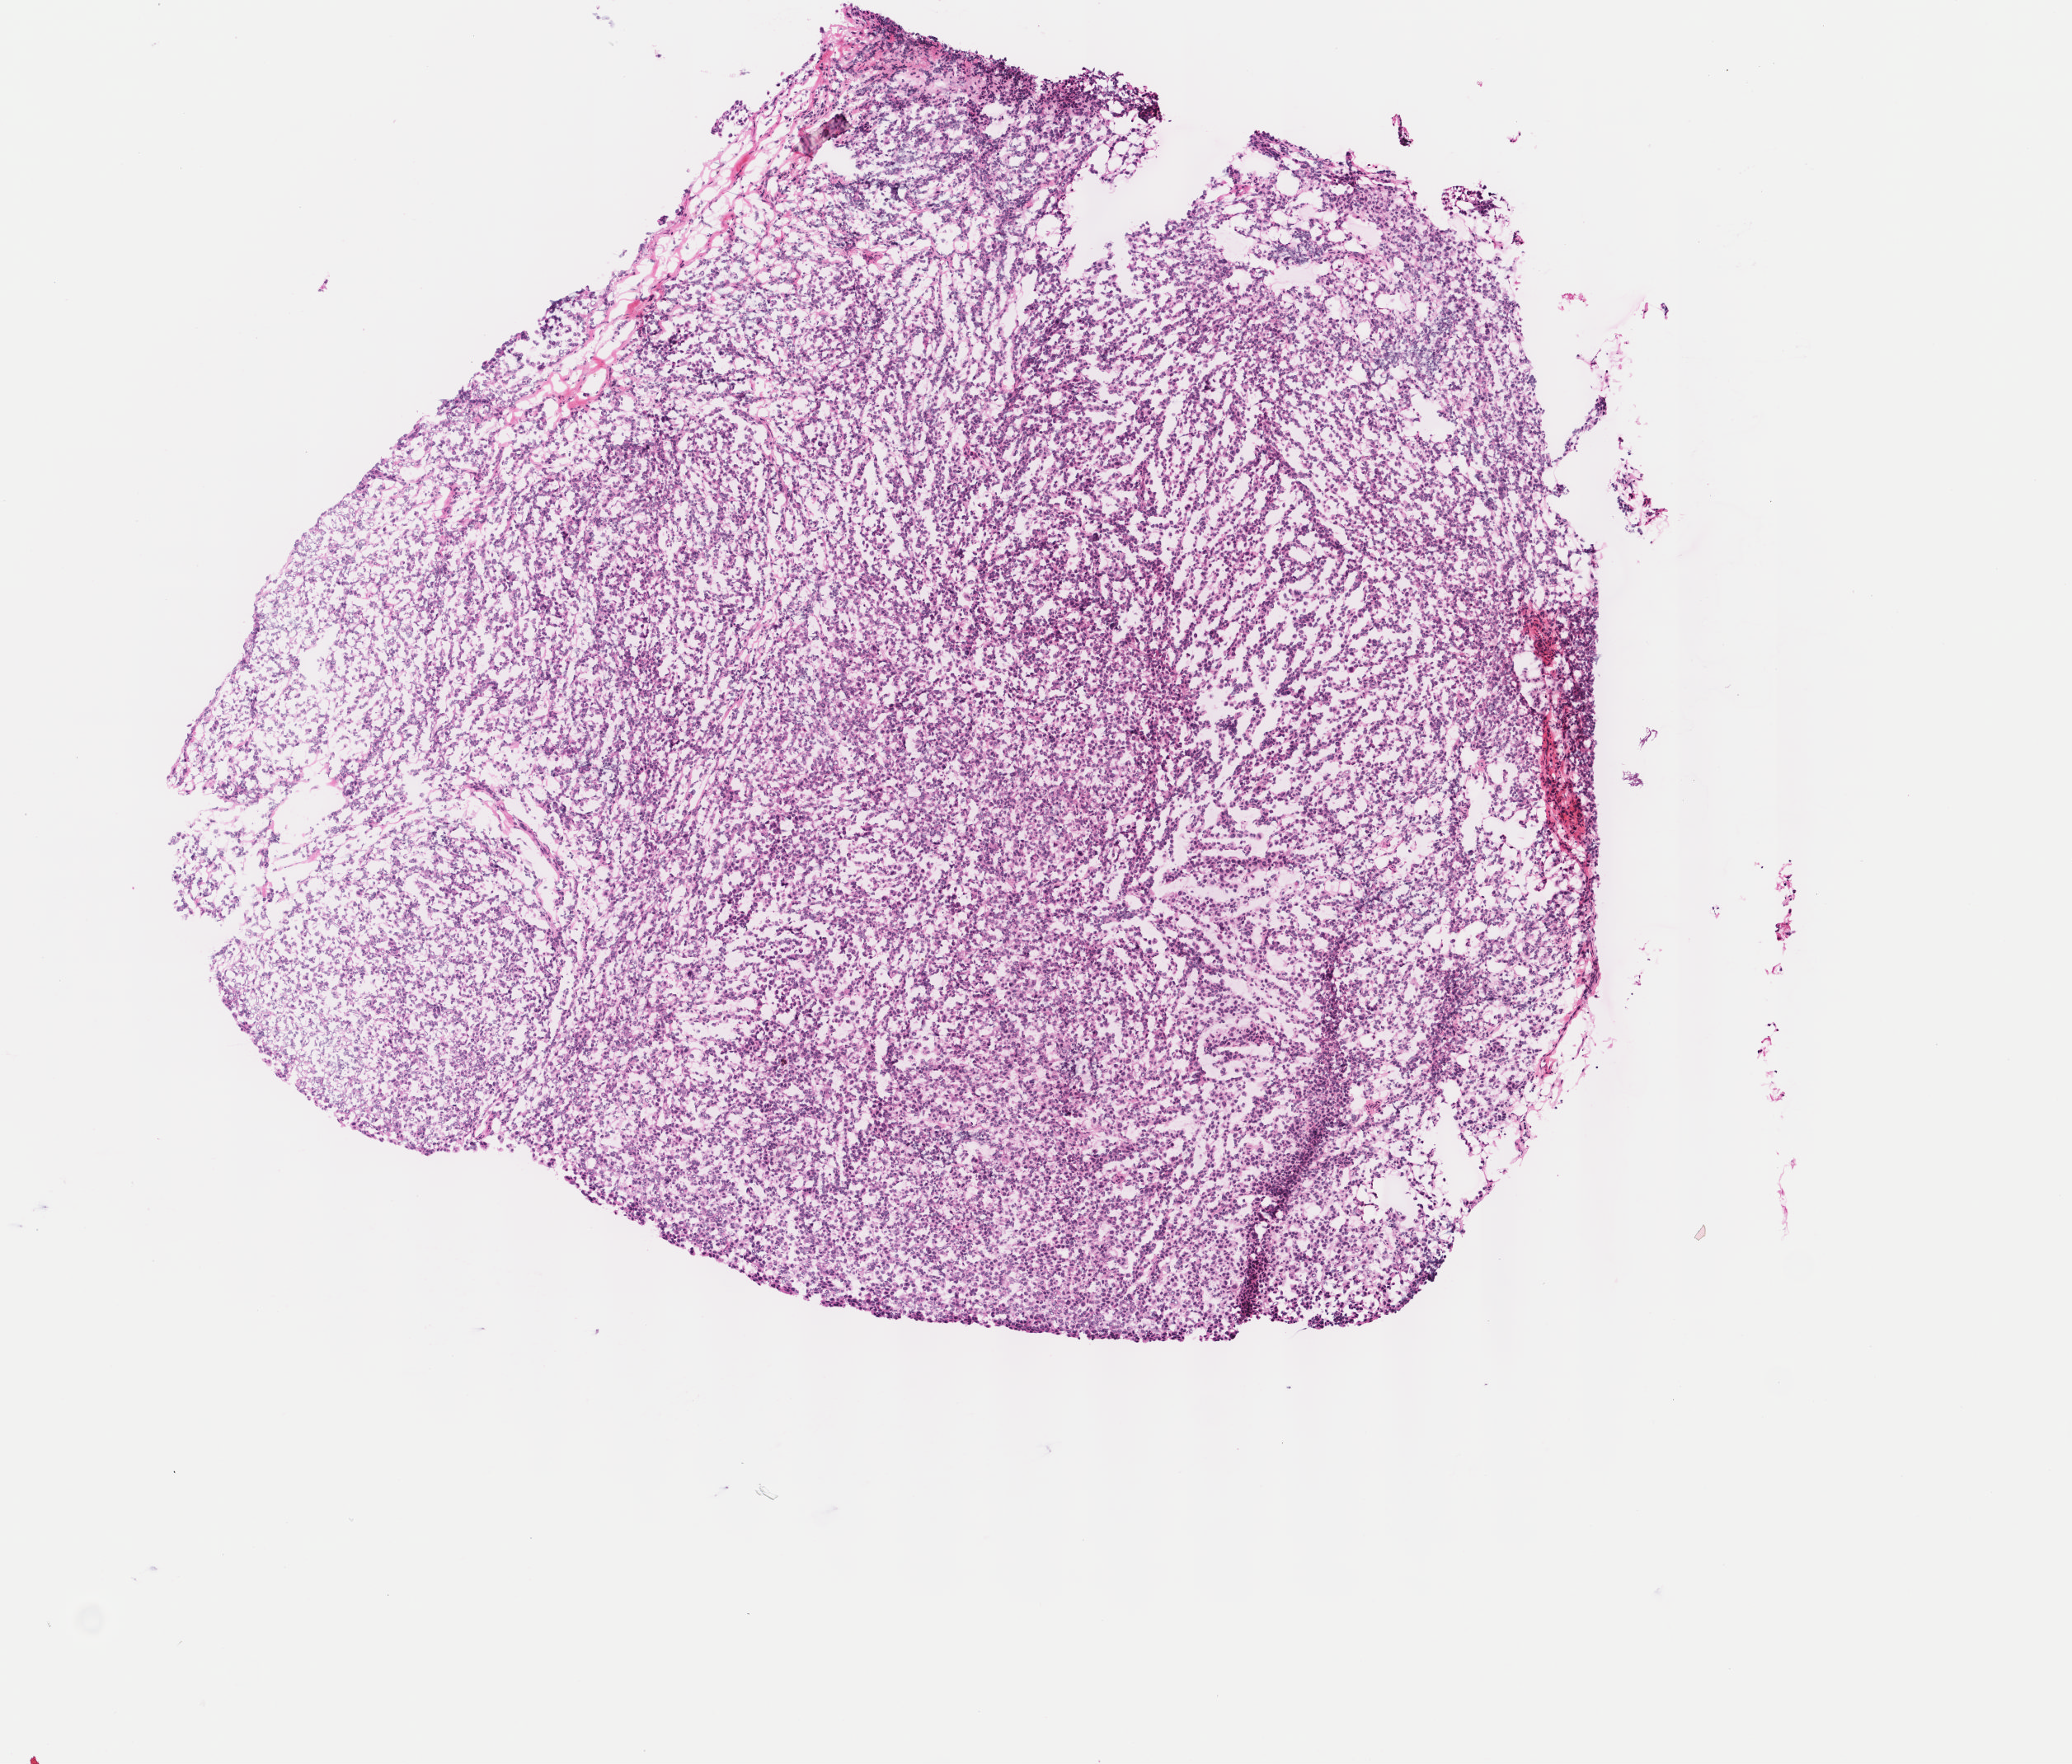
Whole-slide histology image, H&E — low-resolution overview of the scanned area, about 5.0 x 4.3 mm (from a 40x scan). Frozen section from the top of the tissue portion. Metastatic tumour sample, sampled site not recorded. Patient: male, age at initial diagnosis 36 years. Composition of this section per pathologist review: tumour cells 100%, tumour nuclei 95%, normal cells 0%, stromal cells 0%, necrosis 0%. Inflammatory infiltration, as recorded: lymphocyte infiltration 0%, monocyte infiltration 0%, neutrophil infiltration 0%.
• this section: metastatic tumour tissue
• patient diagnosis: Malignant melanoma, NOS